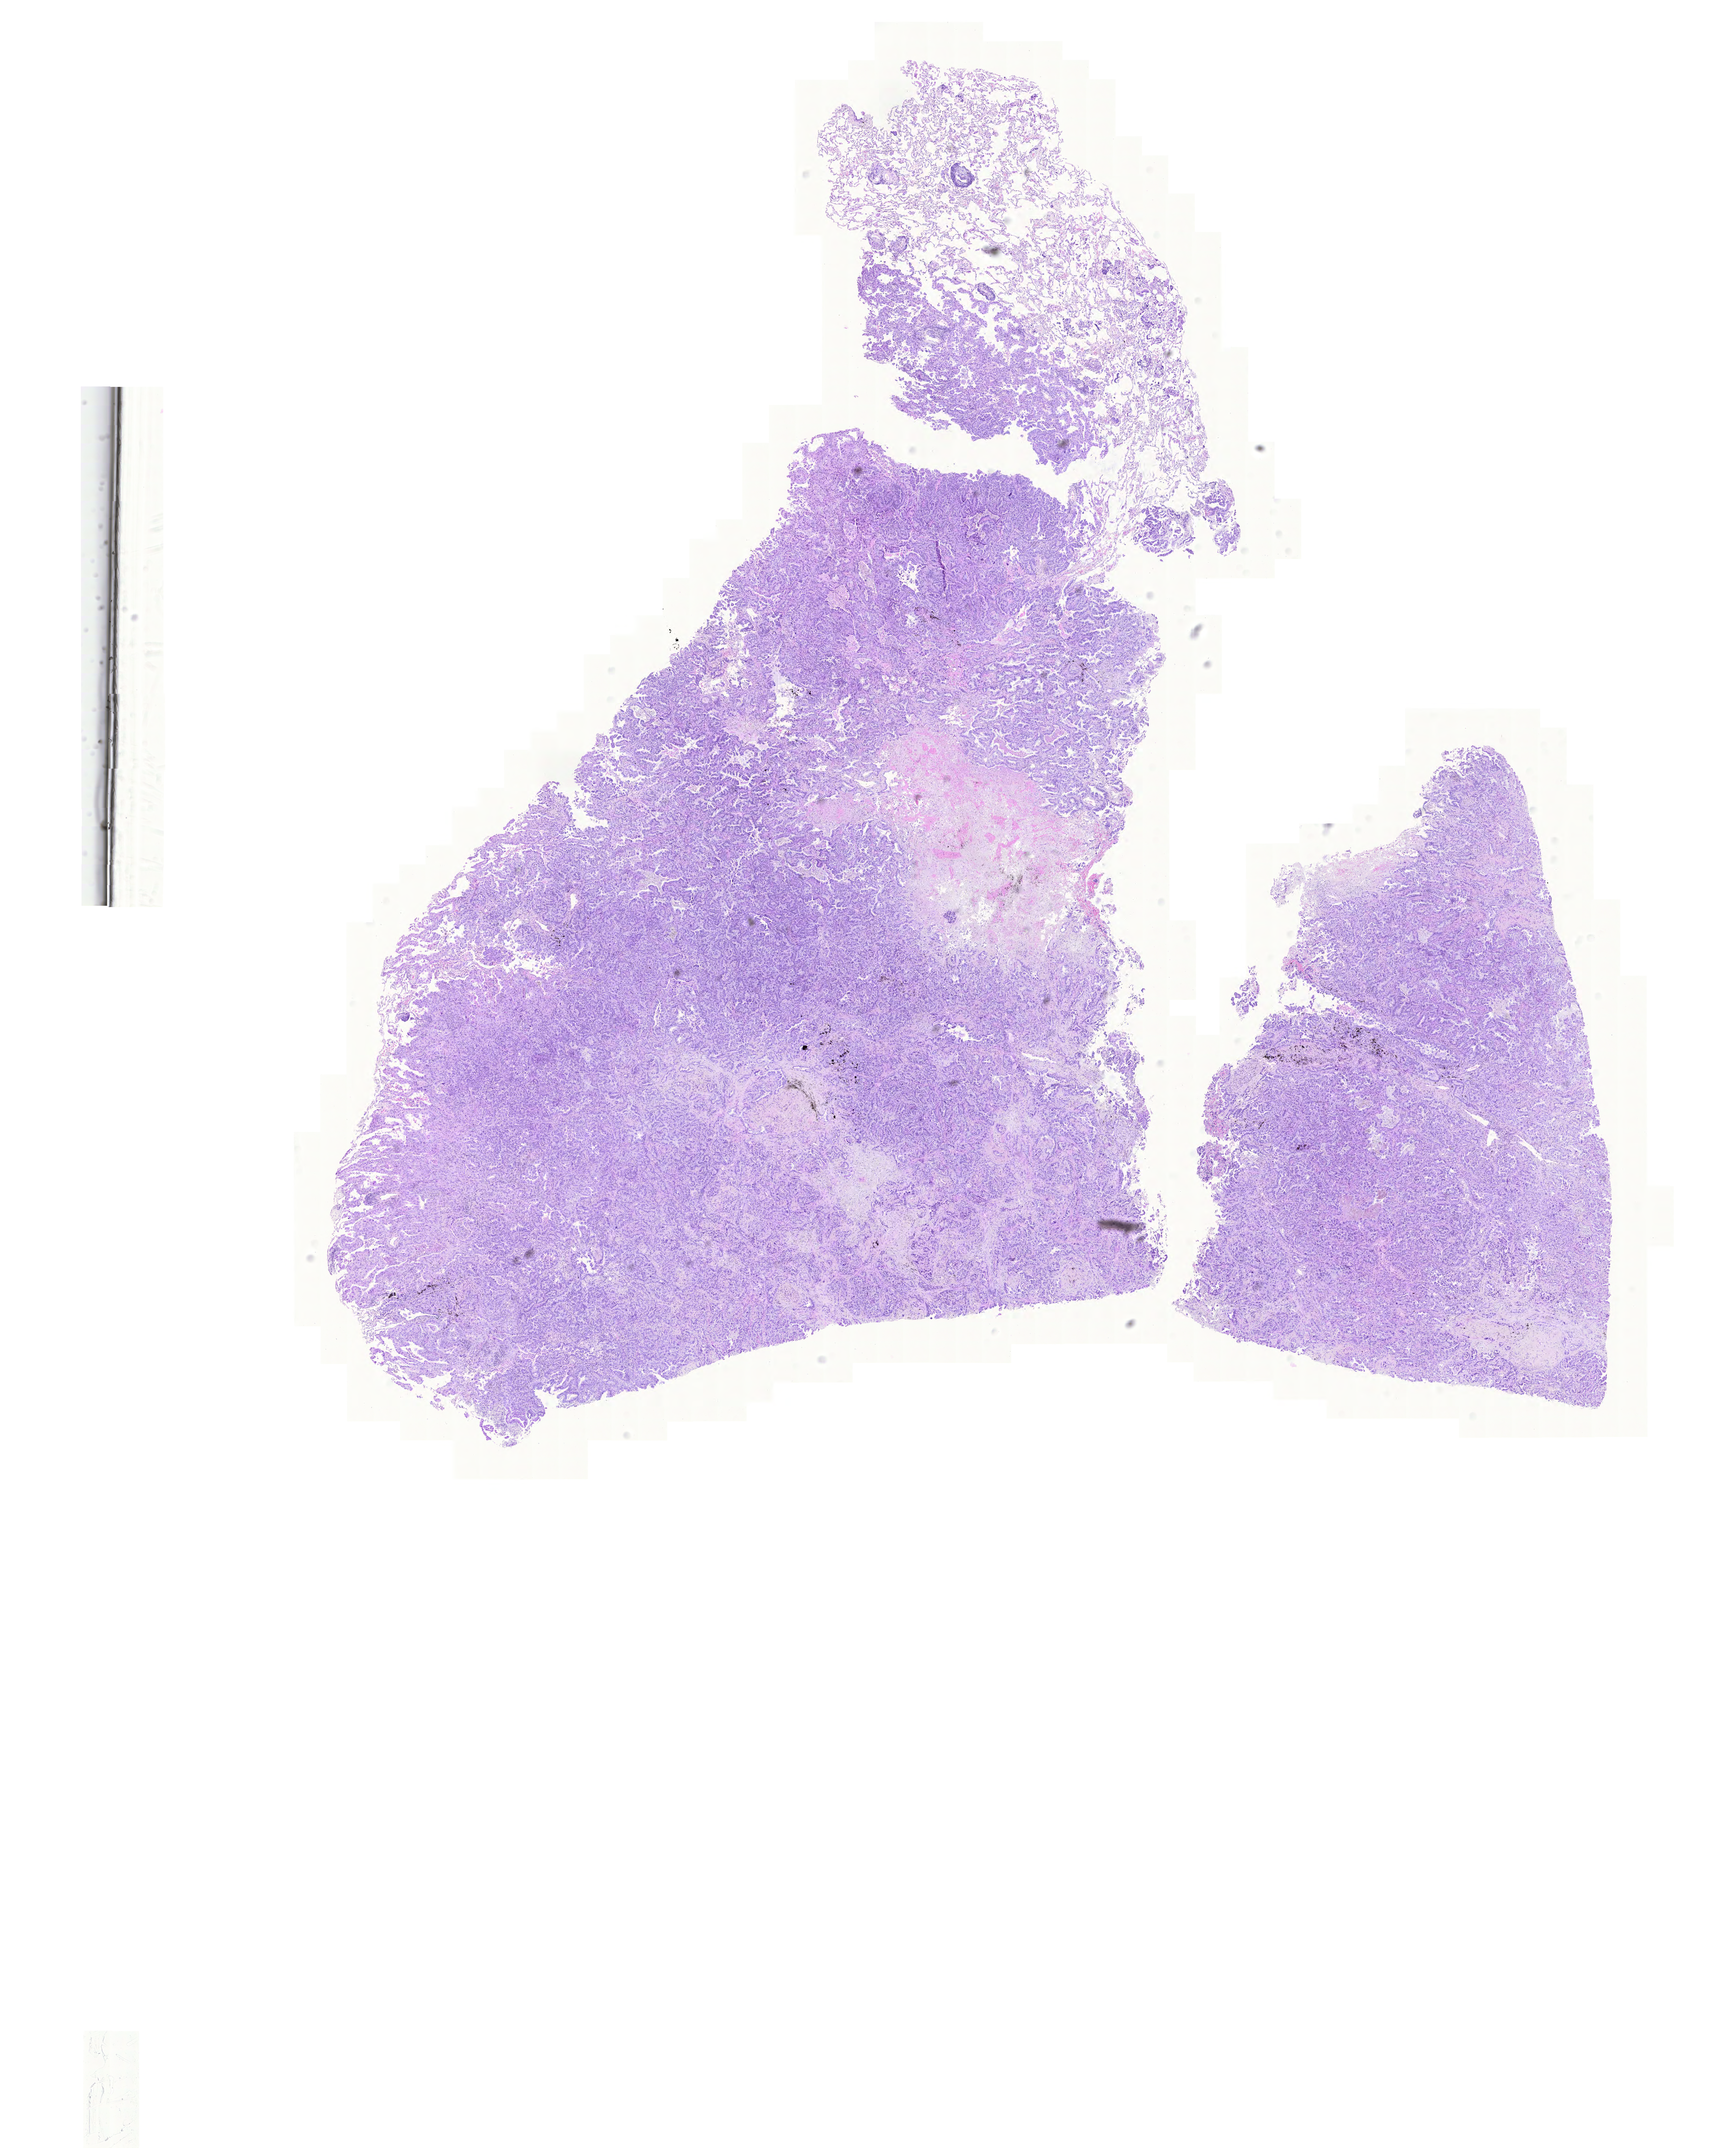
Digitized Hematoxylin and eosin (H&E) stained tissue section (whole slide), whole scanned area (about 18.8 x 23.3 mm) shown as a low-resolution overview, formalin-fixed paraffin-embedded (FFPE) diagnostic section, sample: primary tumour, lung. Female, age 56 years at initial diagnosis.
* diagnosis: Adenocarcinoma with mixed subtypes
* laterality: right
* AJCC pathologic stage: IV (6th edition)